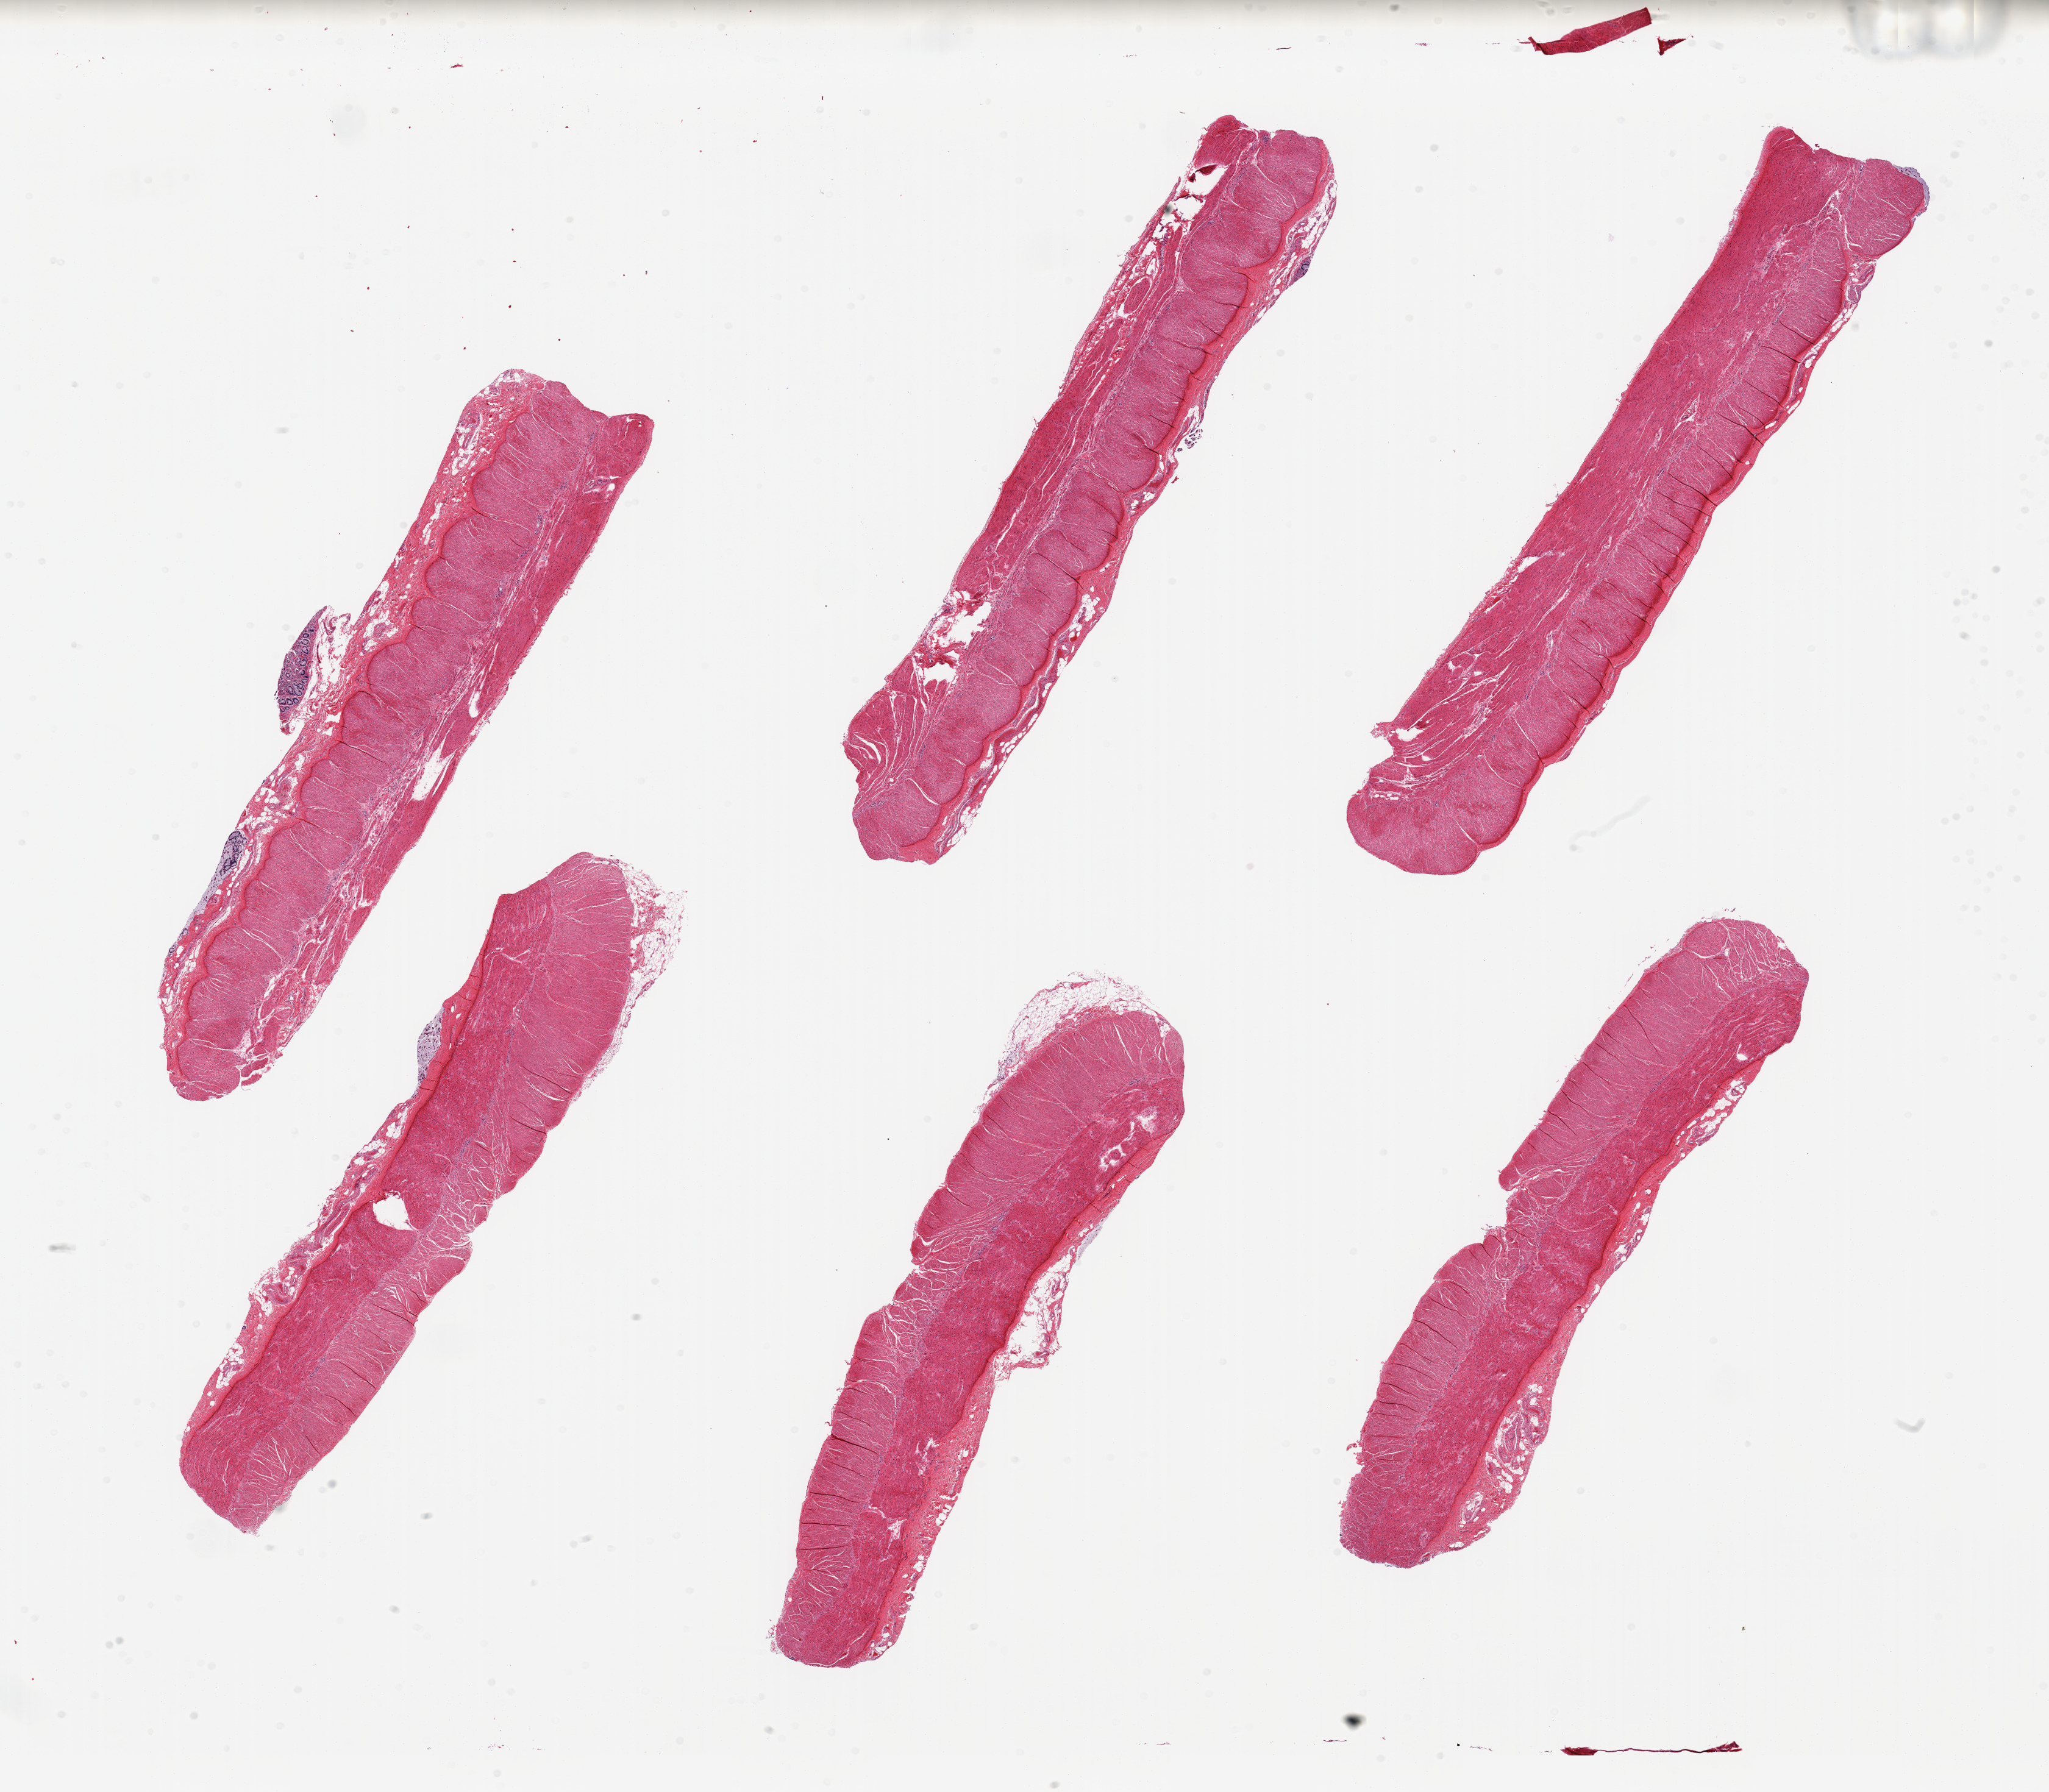
Digitized hematoxylin and eosin (H&E)-stained section — shown as a low-resolution overview of the whole scanned area (about 26.6 x 23.3 mm). PAXgene-fixed, paraffin-embedded tissue. Target tissue: sigmoid colon. Donor tissue sample. Donor: male.
Reviewer comment on this tissue sample: 6 pieces, confirmed target muscularis; focal trace mucosa.